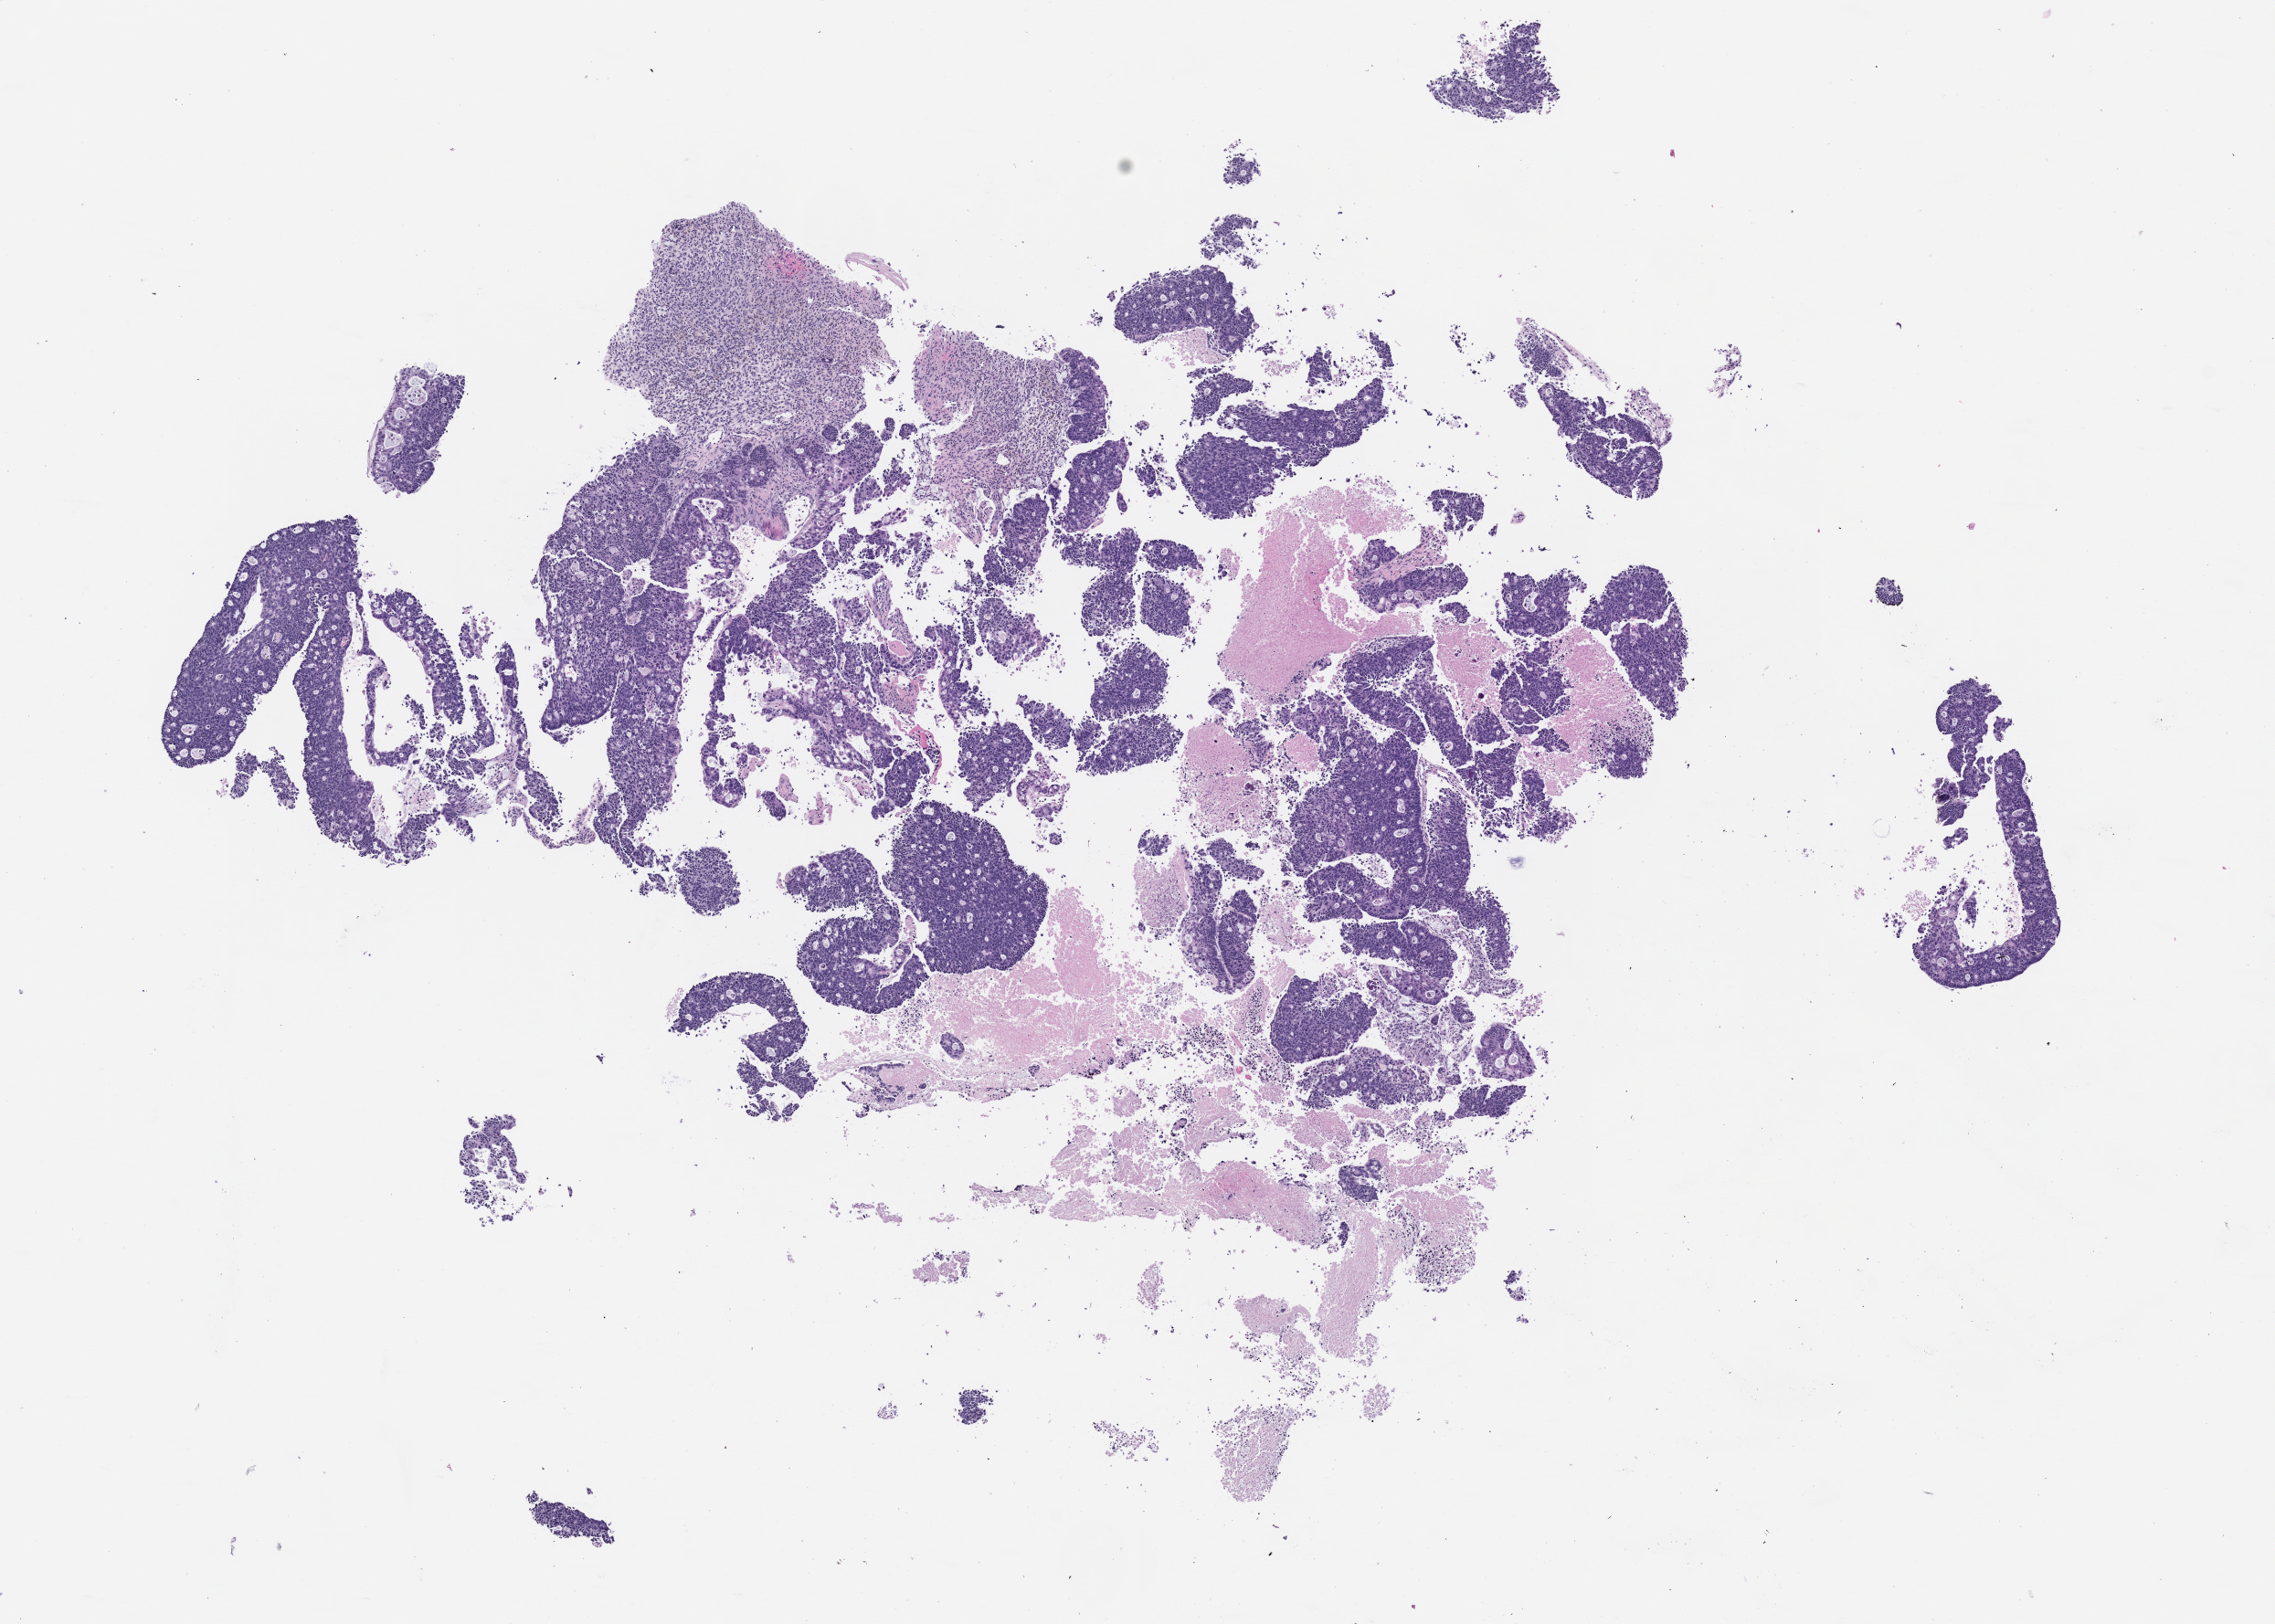
Whole-slide image, hematoxylin and eosin (H&E): patient-derived xenograft (human tumor grown in a mouse), passage 1, shown as a low-resolution overview of the whole scanned area (about 10.0 x 7.2 mm); formalin-fixed paraffin-embedded section; originating tumor site category: rectum.
Originating patient diagnosis: Rectal Adenocarcinoma.